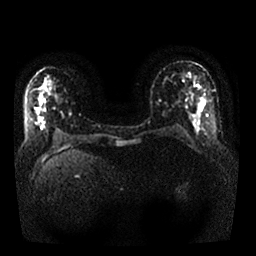
Breast MRI, one axial slice. Position 15 of 25 along the scan axis. Diffusion-weighted series; image 2 of 4 stored at this slice position (different b-values; order by instance number). 1.5 T. 4 mm slice thickness. 256 × 256 image matrix, field of view 340 × 340 mm. Female patient.
Annotated regions visible in this slice (manually delineated by an expert):
- tumour on diffusion-weighted imaging: bounding box <197,104,205,118> (left, top, right, bottom; pixels)